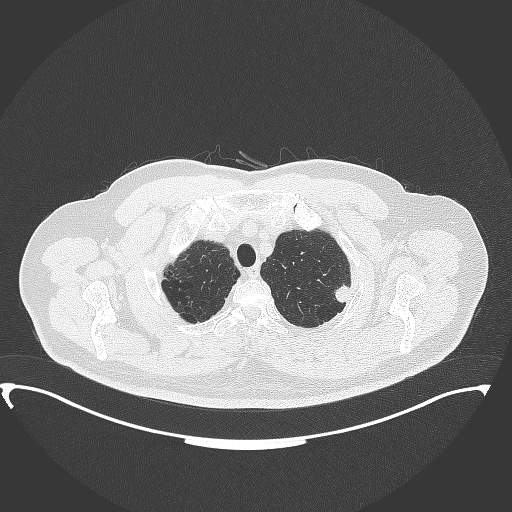
Chest CT, one axial slice. Position 324 of 350 along the scan axis. Lung window (W 1500 / L -600 HU). 1 mm slice thickness. 512 × 512 image matrix. Patient: male, 64 years. From the clinical record (not read from this slice): clinical TNM (as recorded): T1c N1 M1.
Outlined on this slice (bounding box drawn by a radiologist):
- lung tumour (recorded histology: adenocarcinoma): bounding box [x1, y1, x2, y2] px = [333, 278, 354, 305]